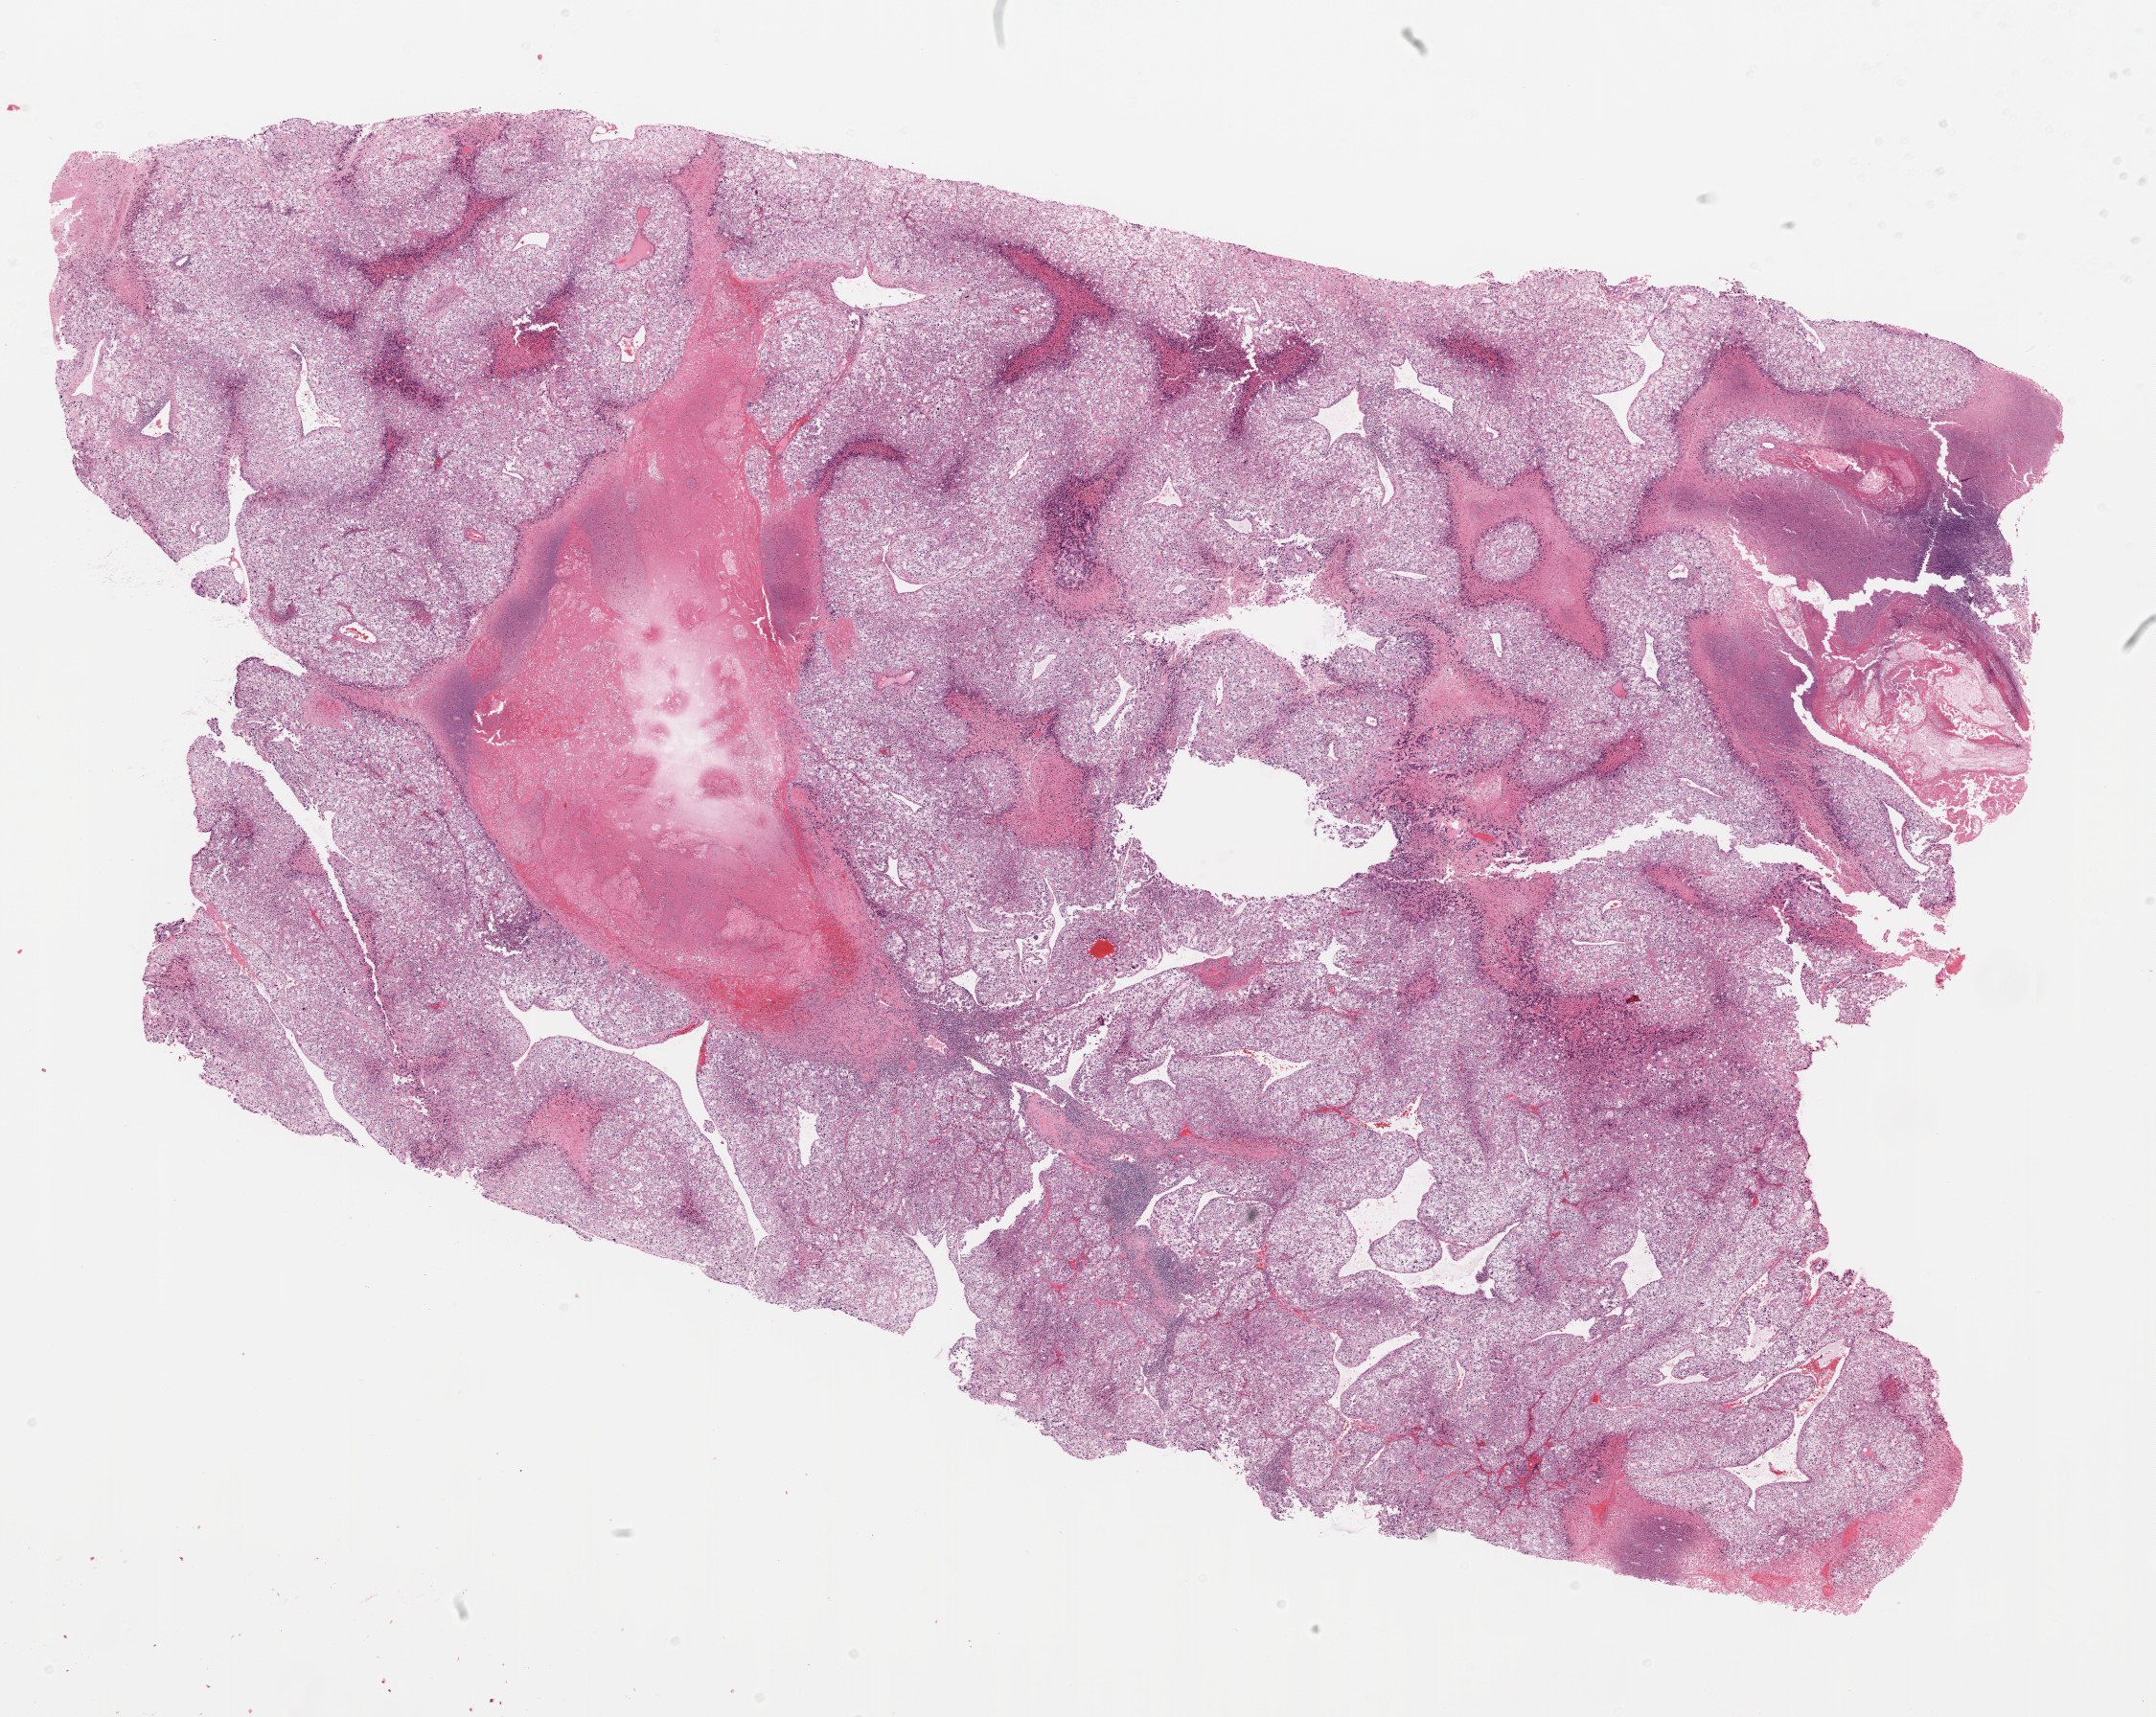
Digitized H&E tissue section (whole slide) — whole scanned area (about 18.1 x 14.4 mm) shown as a low-resolution overview; formalin-fixed paraffin-embedded (FFPE) diagnostic section; kidney, primary tumour sample. Male patient; age at initial diagnosis 39 years. Histologic grade: G4 (undifferentiated).
- pathologic diagnosis: Clear cell adenocarcinoma, NOS
- laterality: left
- AJCC pathologic stage: II